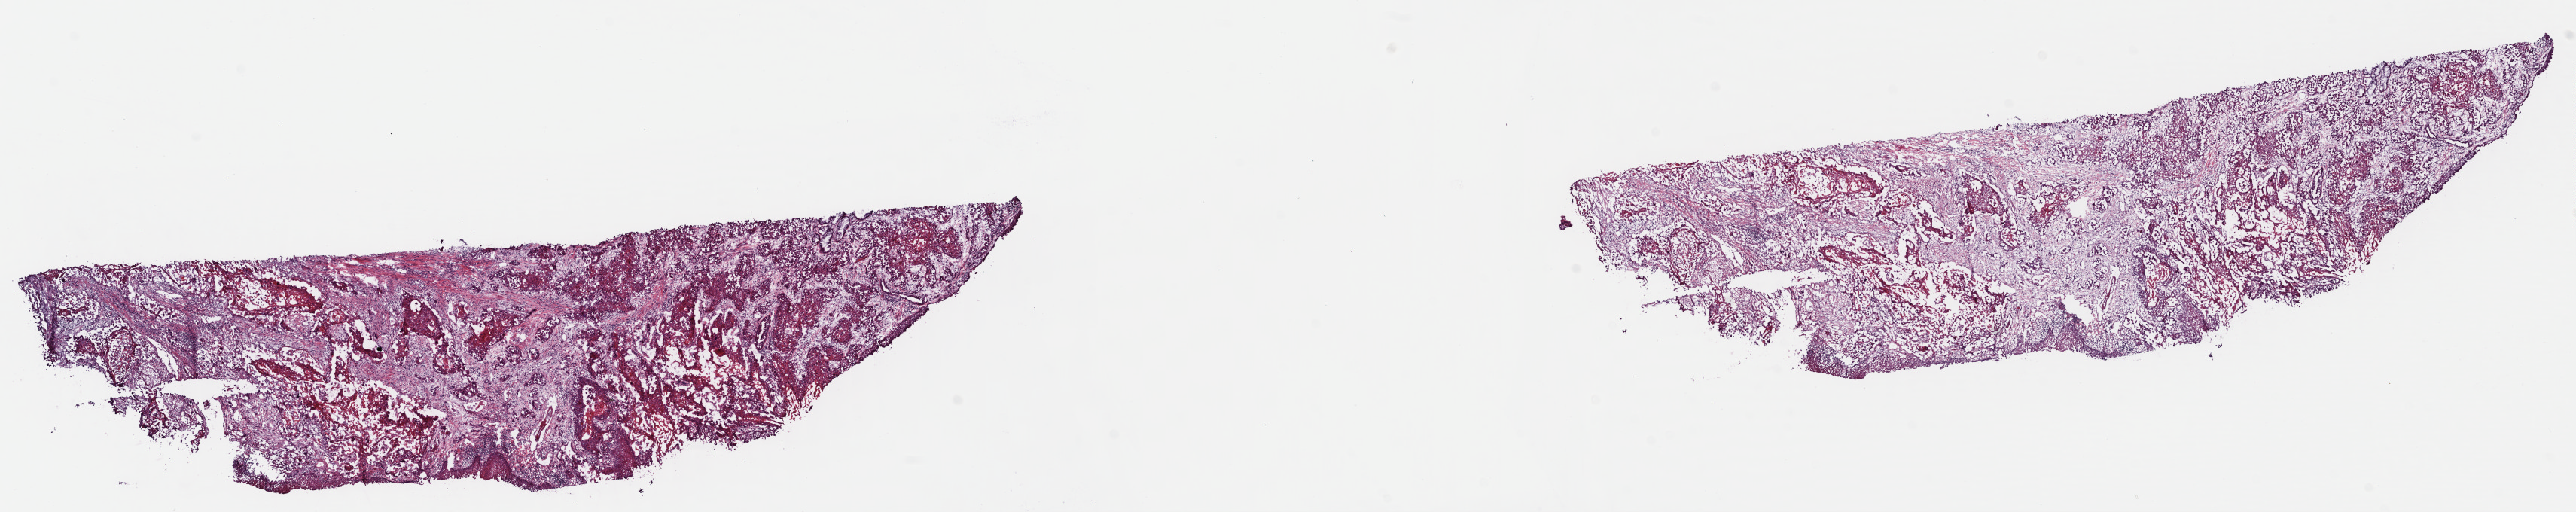
Whole-slide histology image, H&E — low-resolution overview of the scanned area, about 26.9 x 5.3 mm (slide scanned at 40x); frozen section from the top of the tissue portion; primary tumour sample from the head and neck. Male, age 72 years at initial diagnosis. Histologic grade: G2 (moderately differentiated). Composition of this section per pathologist review: tumour cells 45%, tumour nuclei 95%, normal cells 0%, stromal cells 55%, necrosis 0%. Infiltration values recorded for this section: lymphocyte infiltration 6%, monocyte infiltration 5%, neutrophil infiltration 0%.
Diagnosis: Squamous cell carcinoma, NOS (larynx, NOS). AJCC pathologic stage: IVA (7th edition).